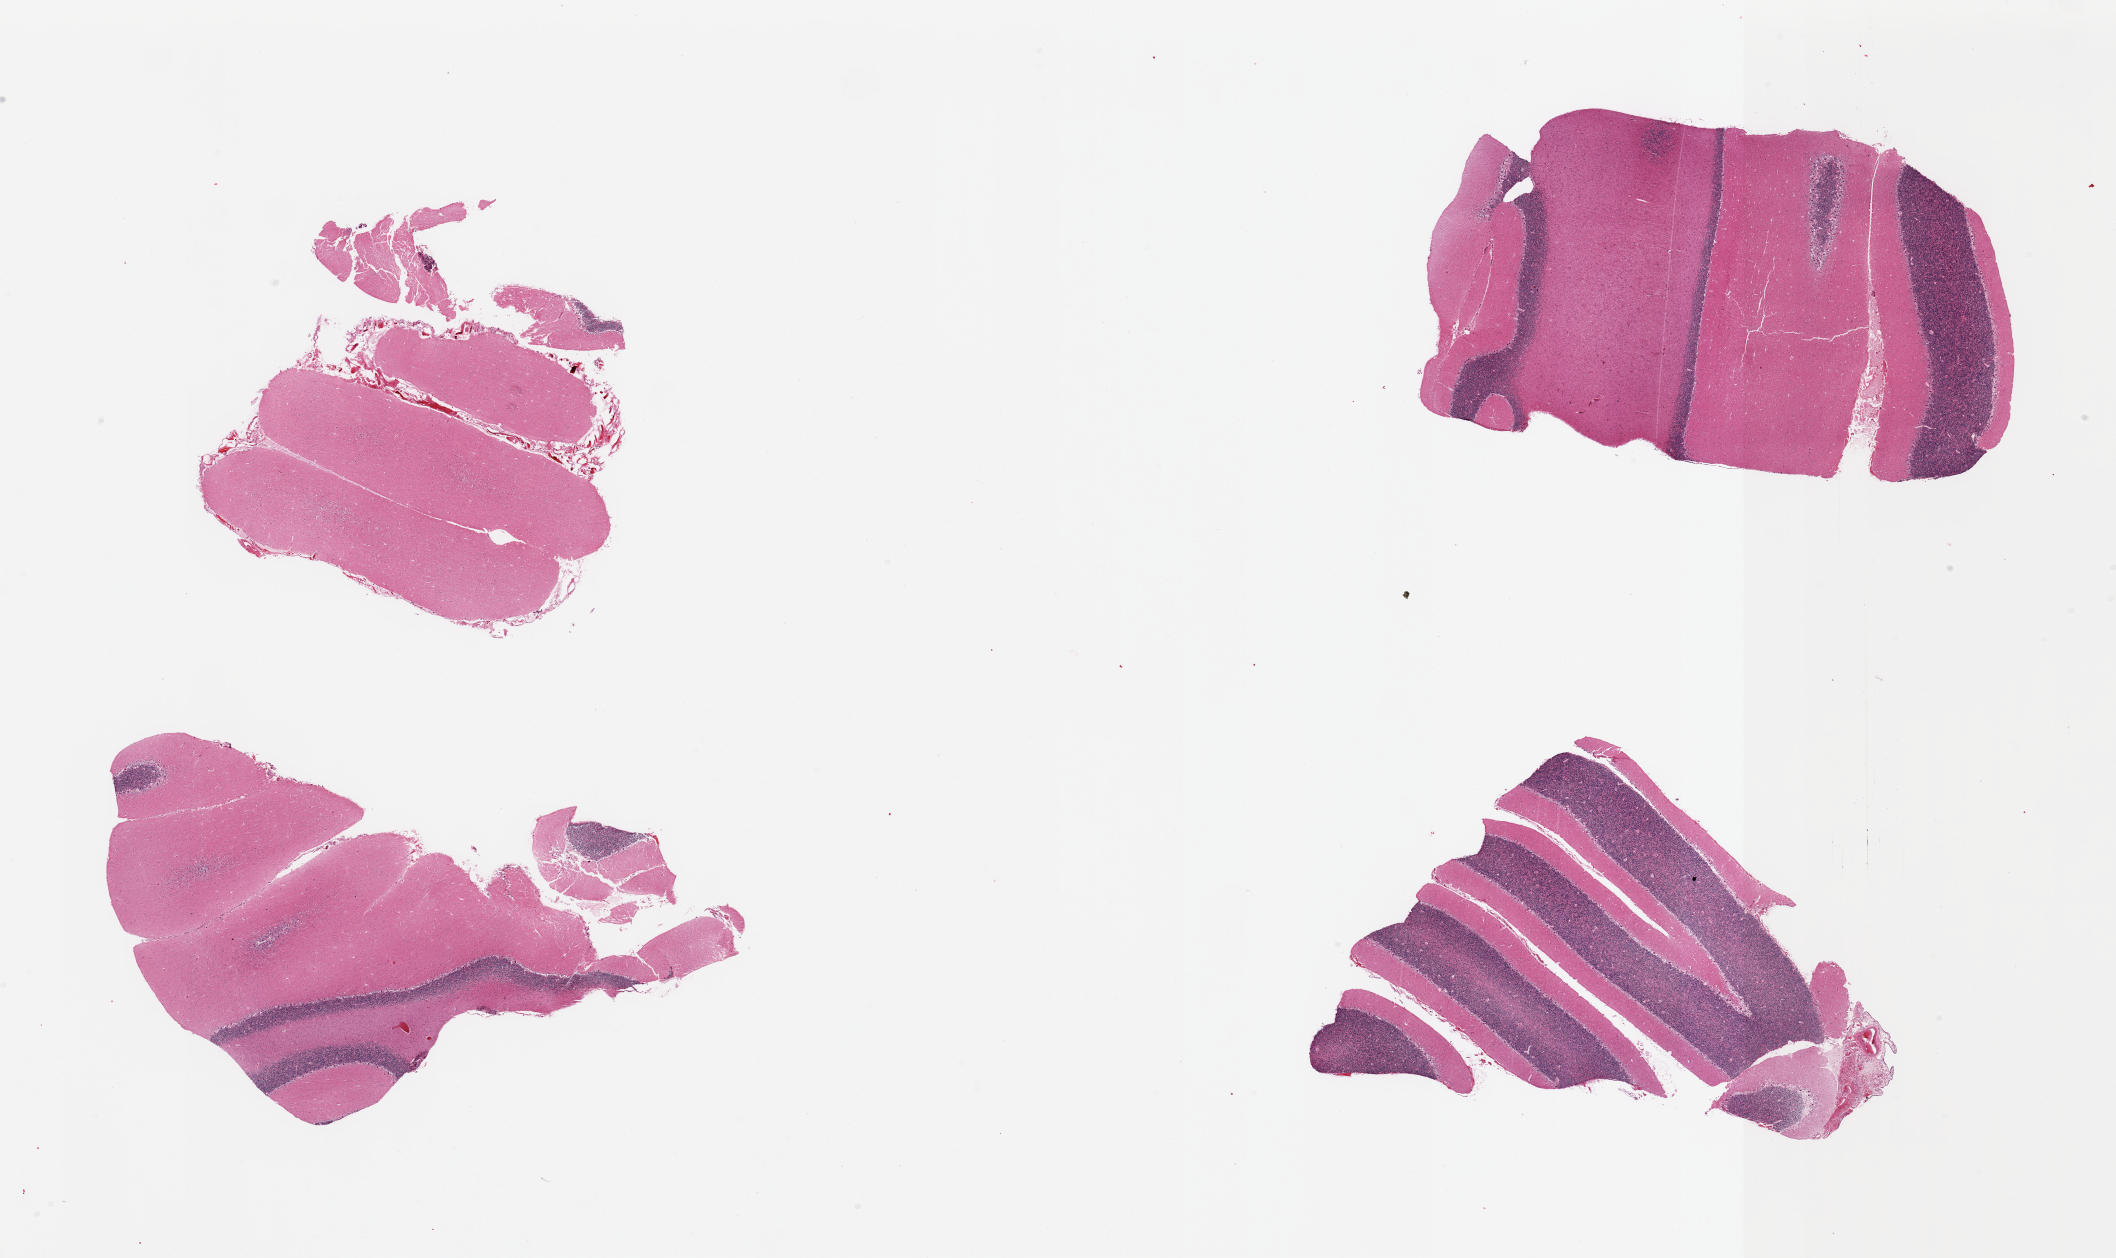
Whole-slide image, H&E stain, low-resolution overview of the scanned area, about 33.5 x 19.9 mm (acquisition: 20x scan); PAXgene-fixed paraffin-embedded (PFPE) section; sampled site (target tissue): cerebellum; donor tissue sample.
Pathologist's review note for this sample: 4 pieces; Purkinje cells present; tiny remnants of meninges.